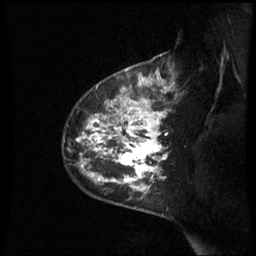
Breast MRI (dynamic contrast-enhanced), one sagittal slice. Slice 46 of 60 in the series (ordered by position). Dynamic contrast-enhanced series, image 2 of 3 at this slice position (ordered by acquisition). 1.5 T. TE 4.2 ms, TR 8.9 ms. 256 × 256 image matrix, field of view 210 × 210 mm. Female patient, age 42 years. From the clinical record (not read from this slice): setting: breast cancer imaged before/during neoadjuvant chemotherapy; receptor status: HER2-positive.
Annotated regions visible in this slice (semi-automatically segmented with operator editing):
- analysis volume of interest (the breast-tissue region the enhancement analysis was run in; not a lesion): box from (x=65, y=93) to (x=170, y=210) px
- tumour enhancement mask (voxels above the 70 % enhancement threshold inside the analysis volume of interest): (x=78, y=100)–(x=168, y=192)